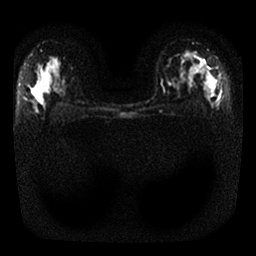
Breast MRI, one axial slice. Slice 20 of 25 in the series (ordered by position). Diffusion-weighted series; image 2 of 4 stored at this slice position (different b-values; order by instance number). 1.5 T. 256 × 256 image matrix, field of view 320 × 320 mm. Female patient.
Annotated regions visible in this slice (expert manual segmentation):
- tumour on diffusion-weighted imaging: bounding box [x1, y1, x2, y2] px = [200, 60, 215, 95]